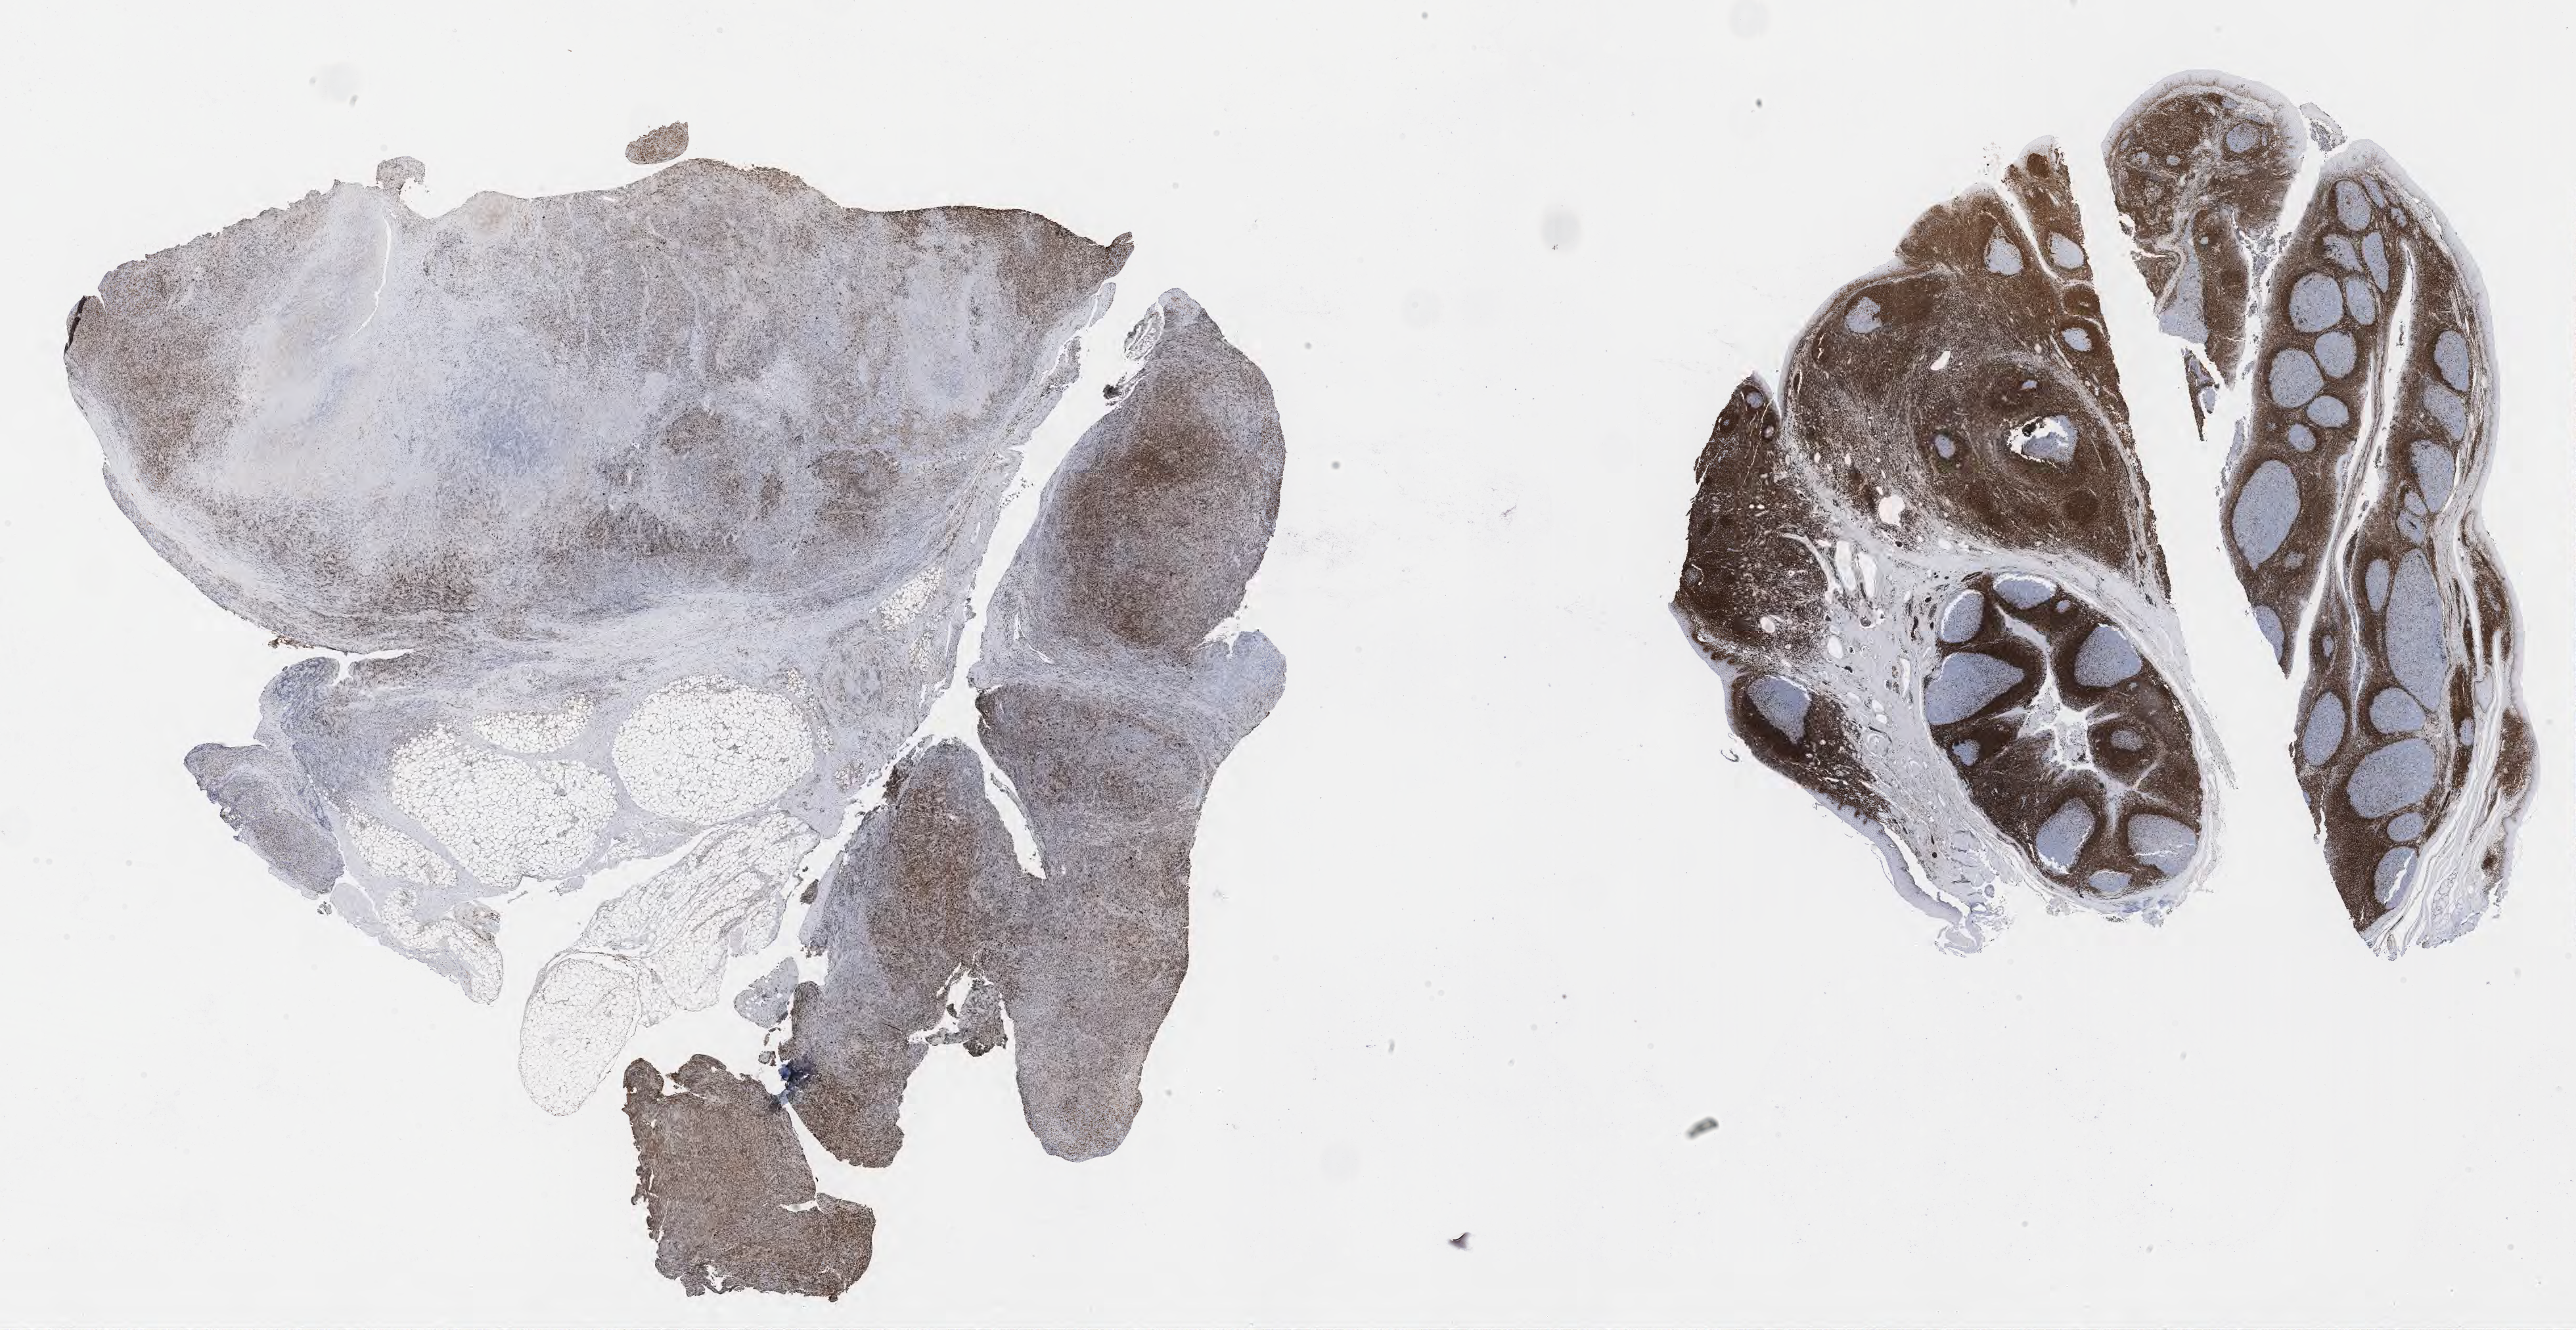
Whole-slide image, immunohistochemical stain for BCL2, whole scanned area (about 31.7 x 16.4 mm) shown as a low-resolution overview. Tumor tissue. Female patient, aged 46.
Histologic diagnosis: Diffuse large B-cell lymphoma, NOS.